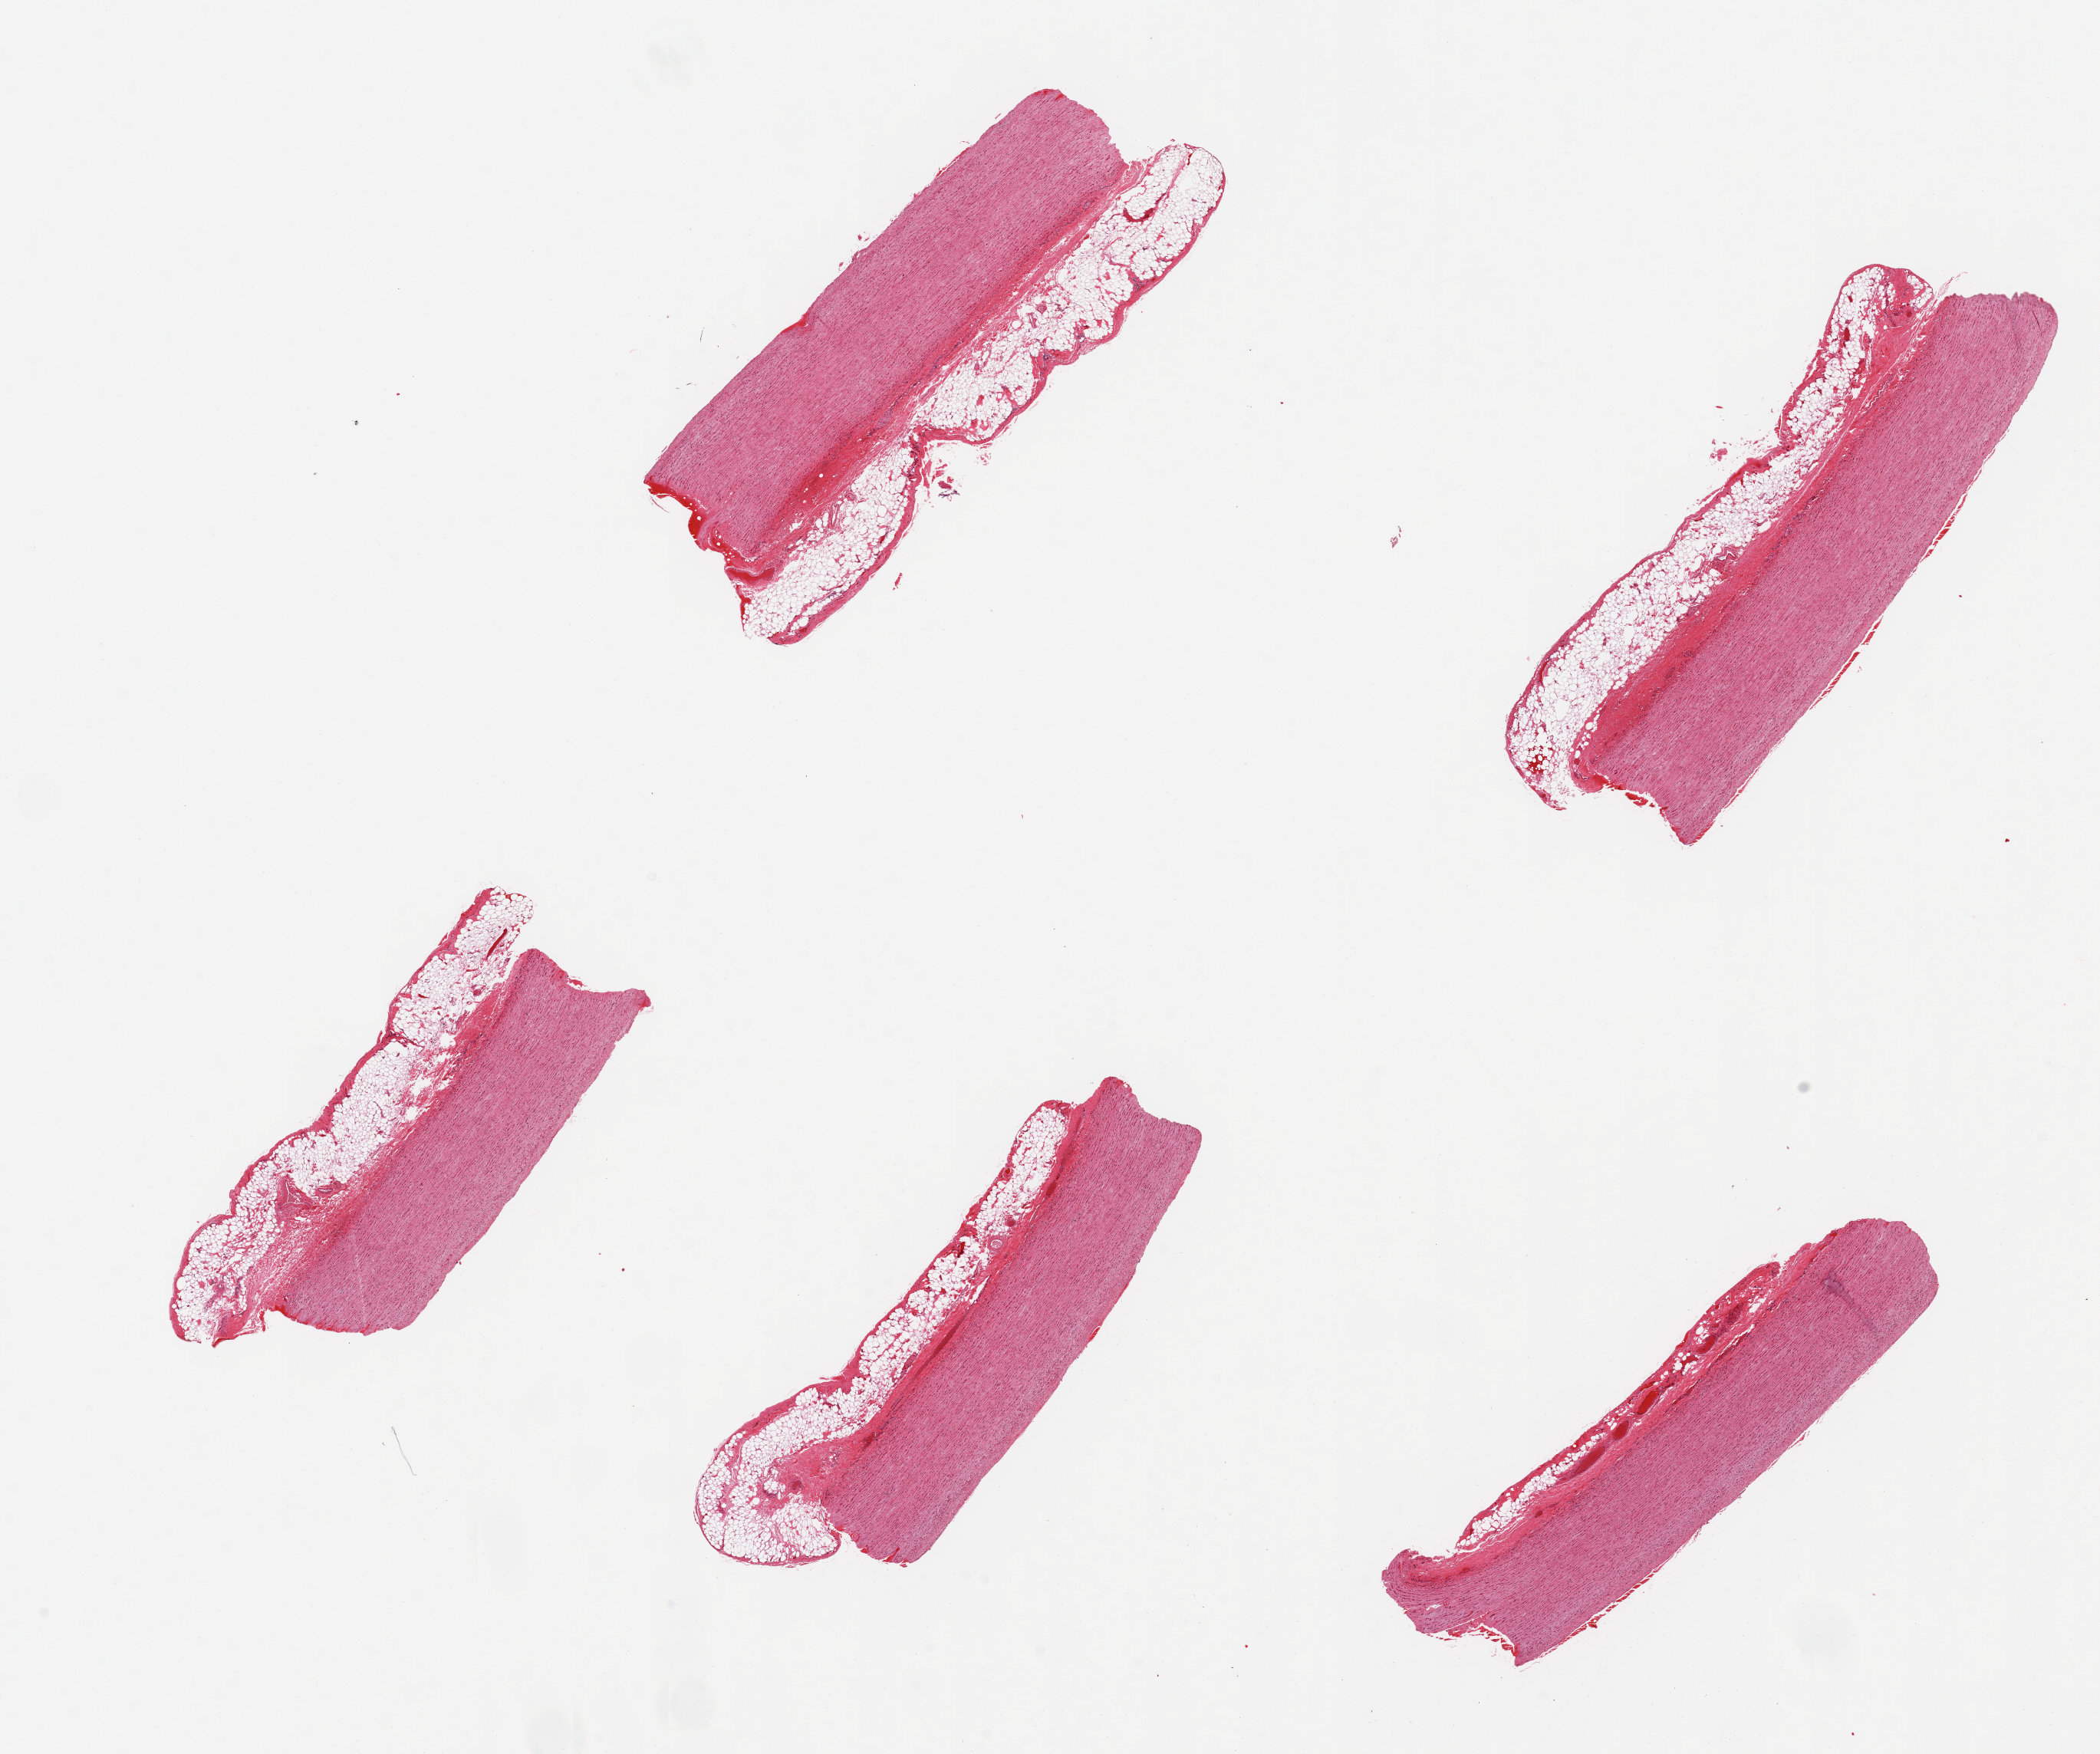
Digitized haematoxylin and eosin-stained section, shown as a low-resolution overview of the whole scanned area (about 21.7 x 18.1 mm, acquisition: 20x scan); PAXgene-fixed paraffin-embedded (PFPE) section; target tissue: aorta; donor tissue sample. Donor: male.
Pathologist's review note for this sample: 5 pieces; all have thick periaortic adventitial adipose layers measuring up to 1 mm.